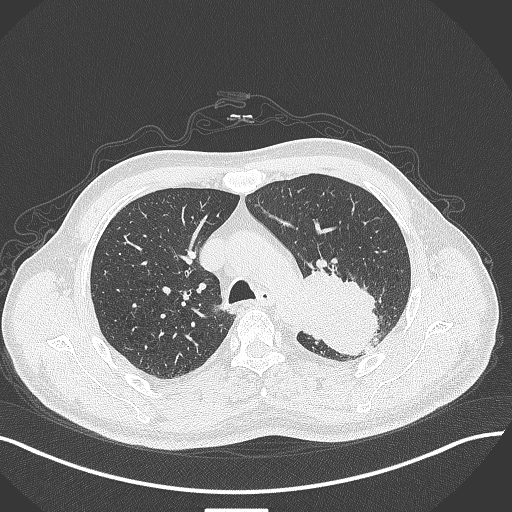
Chest CT, one axial slice; slice 304 of 429 in the series (ordered by position); reconstruction kernel B70f; 120 kVp; lung window (W 1500 / L -600 HU); 1 mm slice thickness; 512 × 512 image matrix. Patient: male, 55 years. From the clinical record (not read from this slice): clinical TNM (as recorded): T3 N0 M1c; histopathological grade: G3.
Structures marked on this image (bounding box drawn by a radiologist):
- lung tumour (recorded histology: adenocarcinoma): box from (x=296, y=264) to (x=382, y=361) px